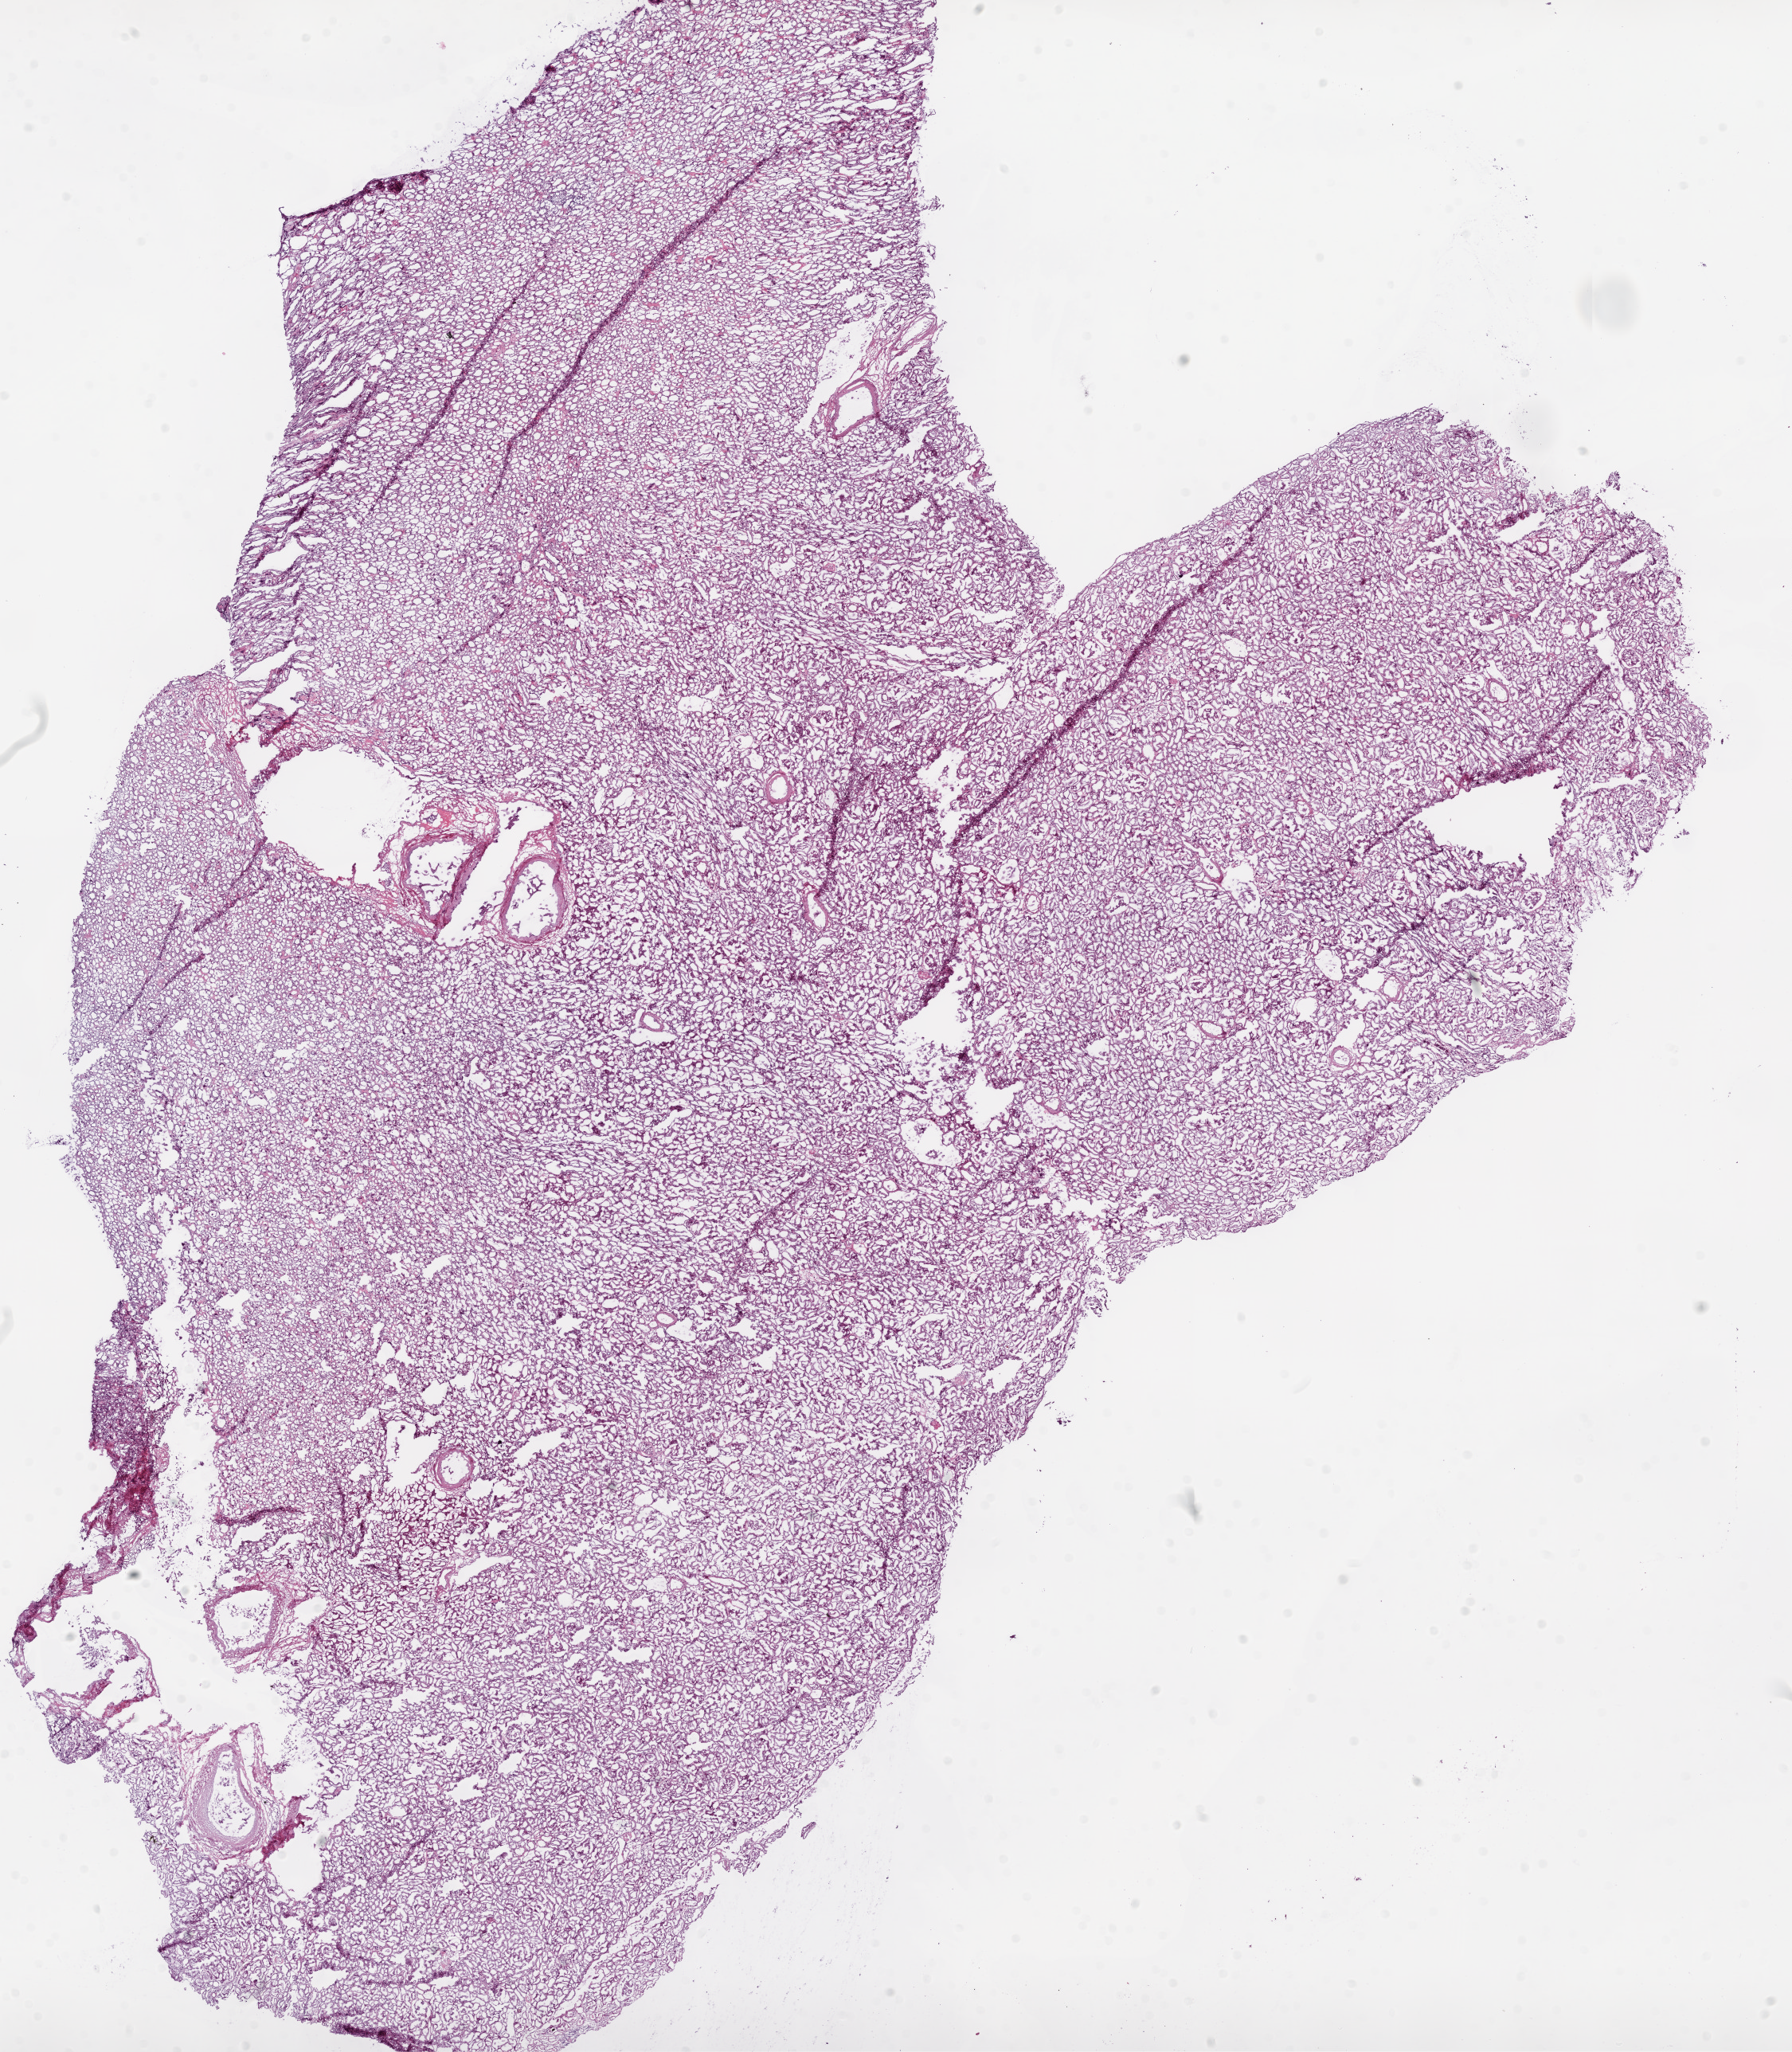
H&E-stained whole-slide image, a low-resolution overview of the entire scanned area, about 18.1 x 20.7 mm. Frozen section from the bottom of the tissue portion. Sample: solid tissue normal (non-tumour tissue), kidney. Female patient; age at initial diagnosis 74 years.
This section: solid tissue normal sample (biorepository sample class). Patient diagnosis: Clear cell adenocarcinoma, NOS.